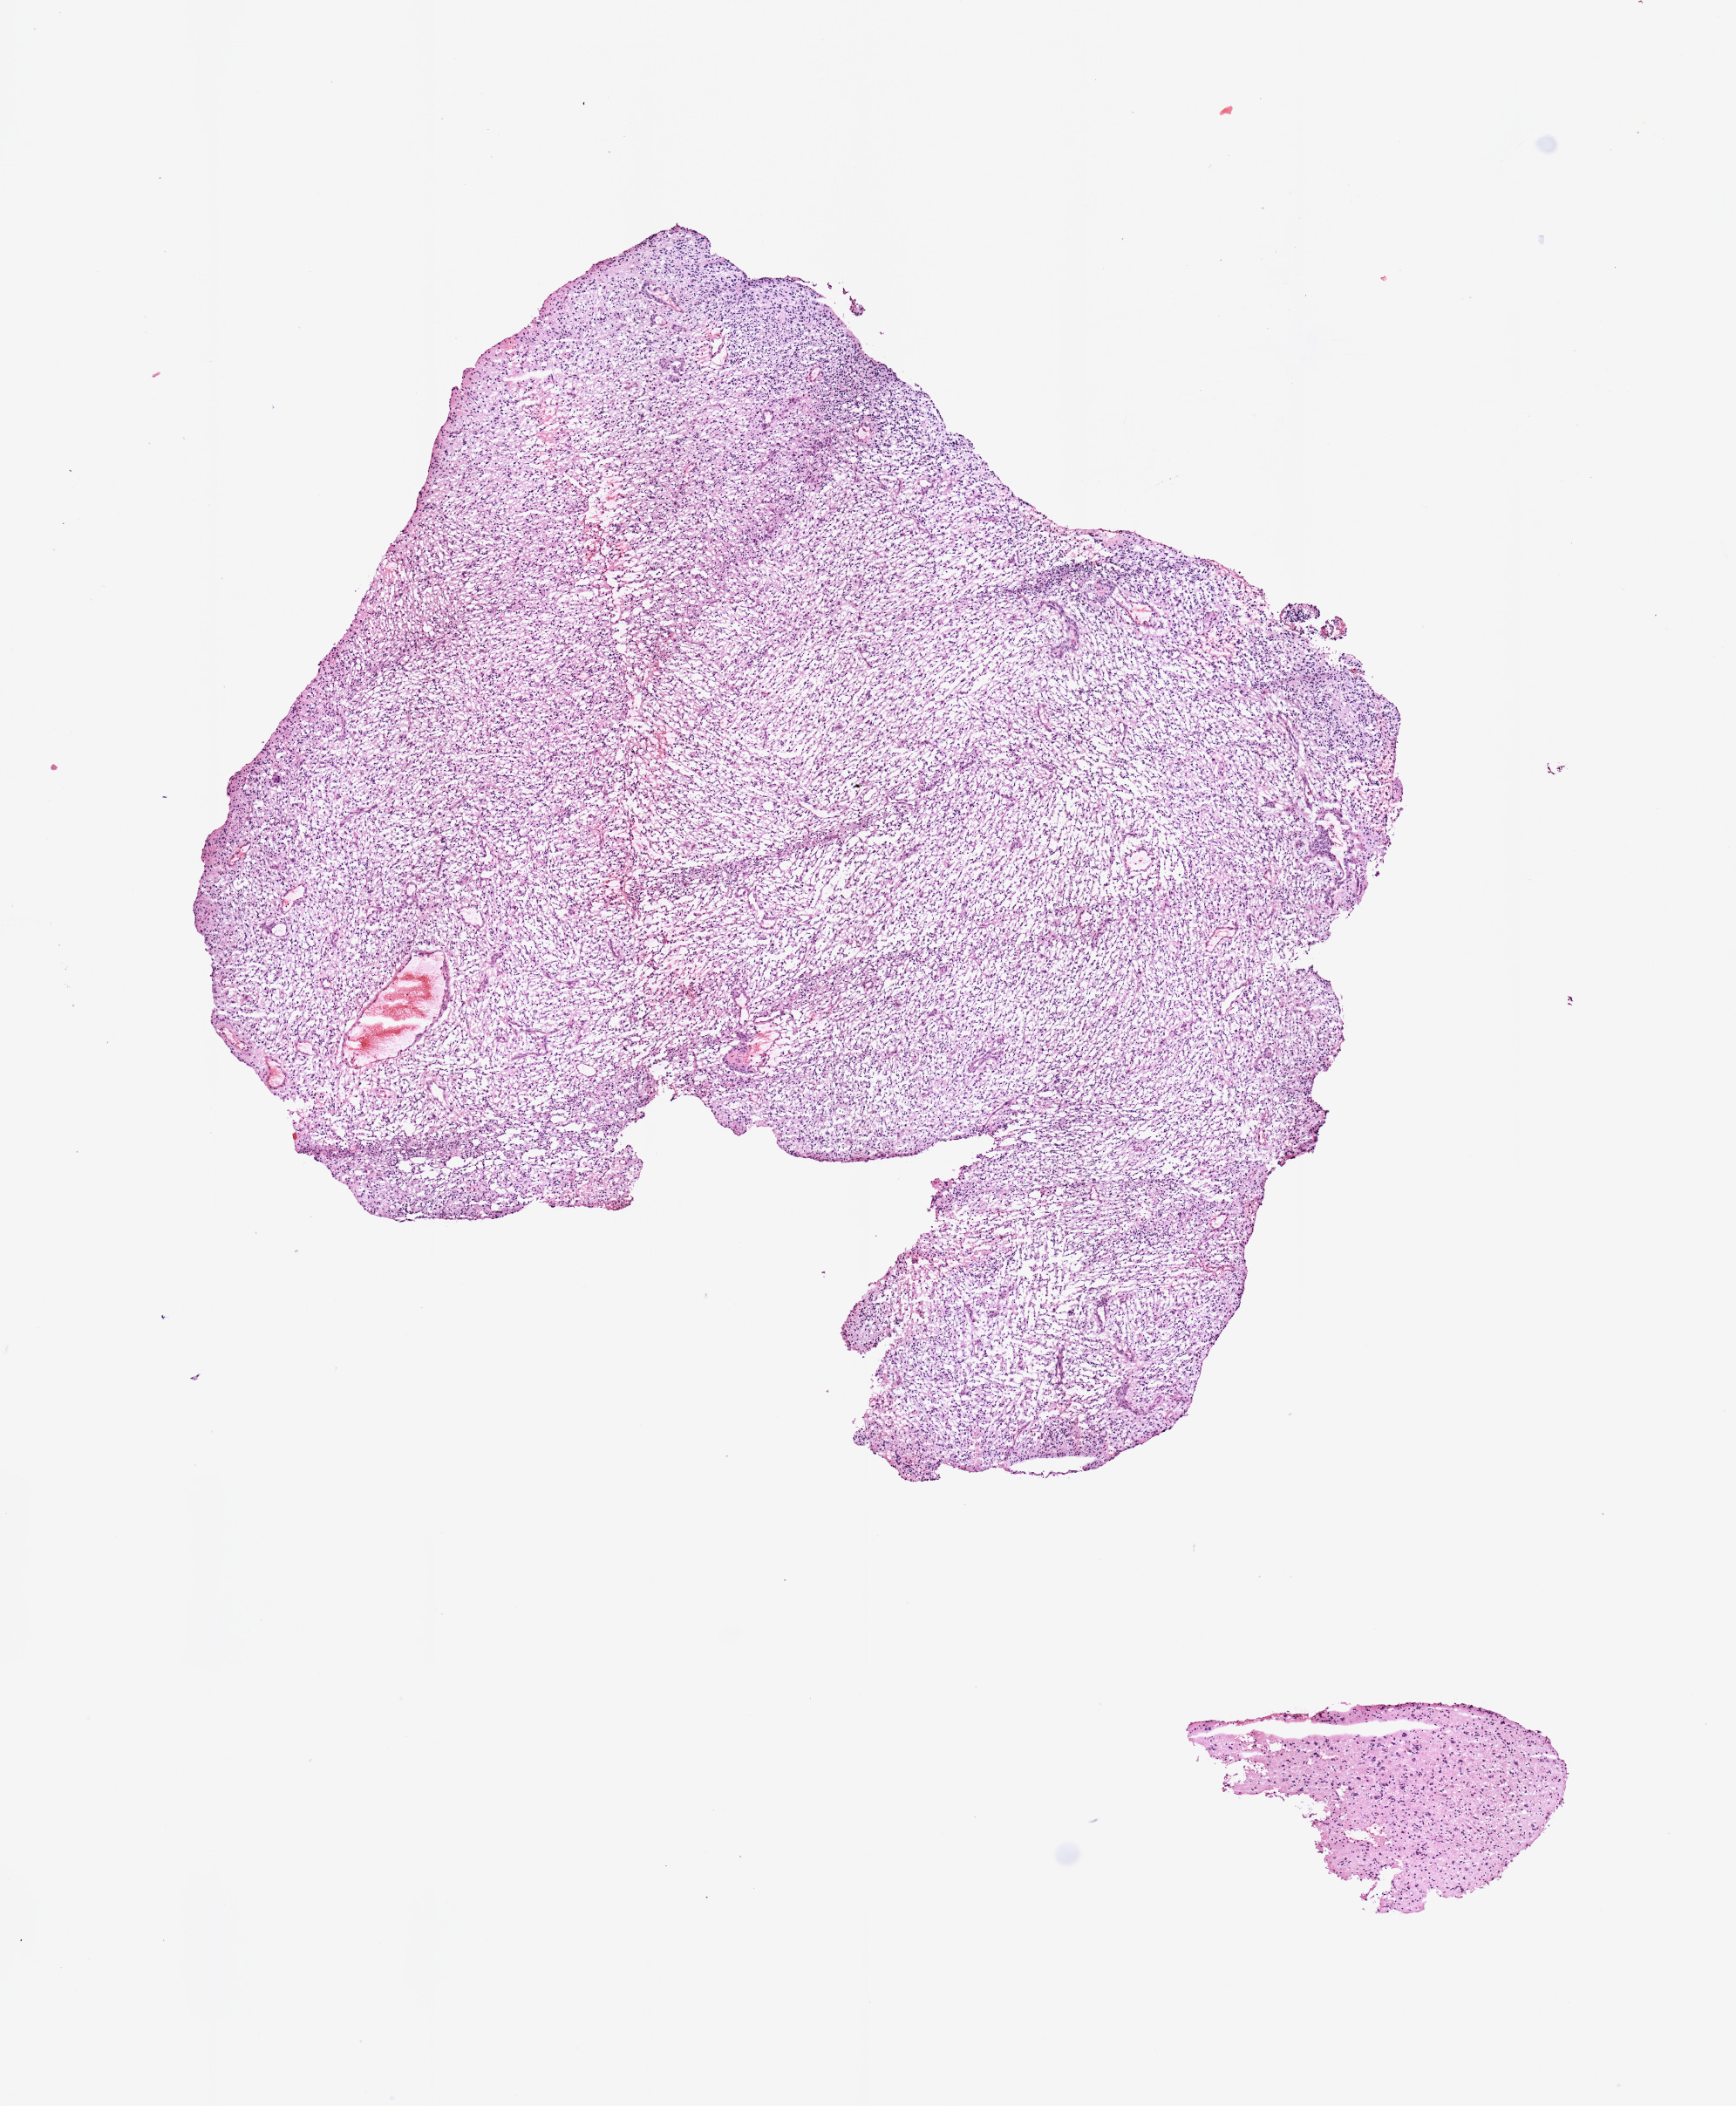
Whole-slide histology image, H&E-stained — low-resolution overview of the scanned area, about 7.9 x 9.6 mm (slide scanned at 20x); tumour tissue sample, brain. Patient: male, age 65 years.
Primary tumour site (as recorded): left hemisphere. Patient diagnosis (cohort enrolment): glioblastoma multiforme (brain).